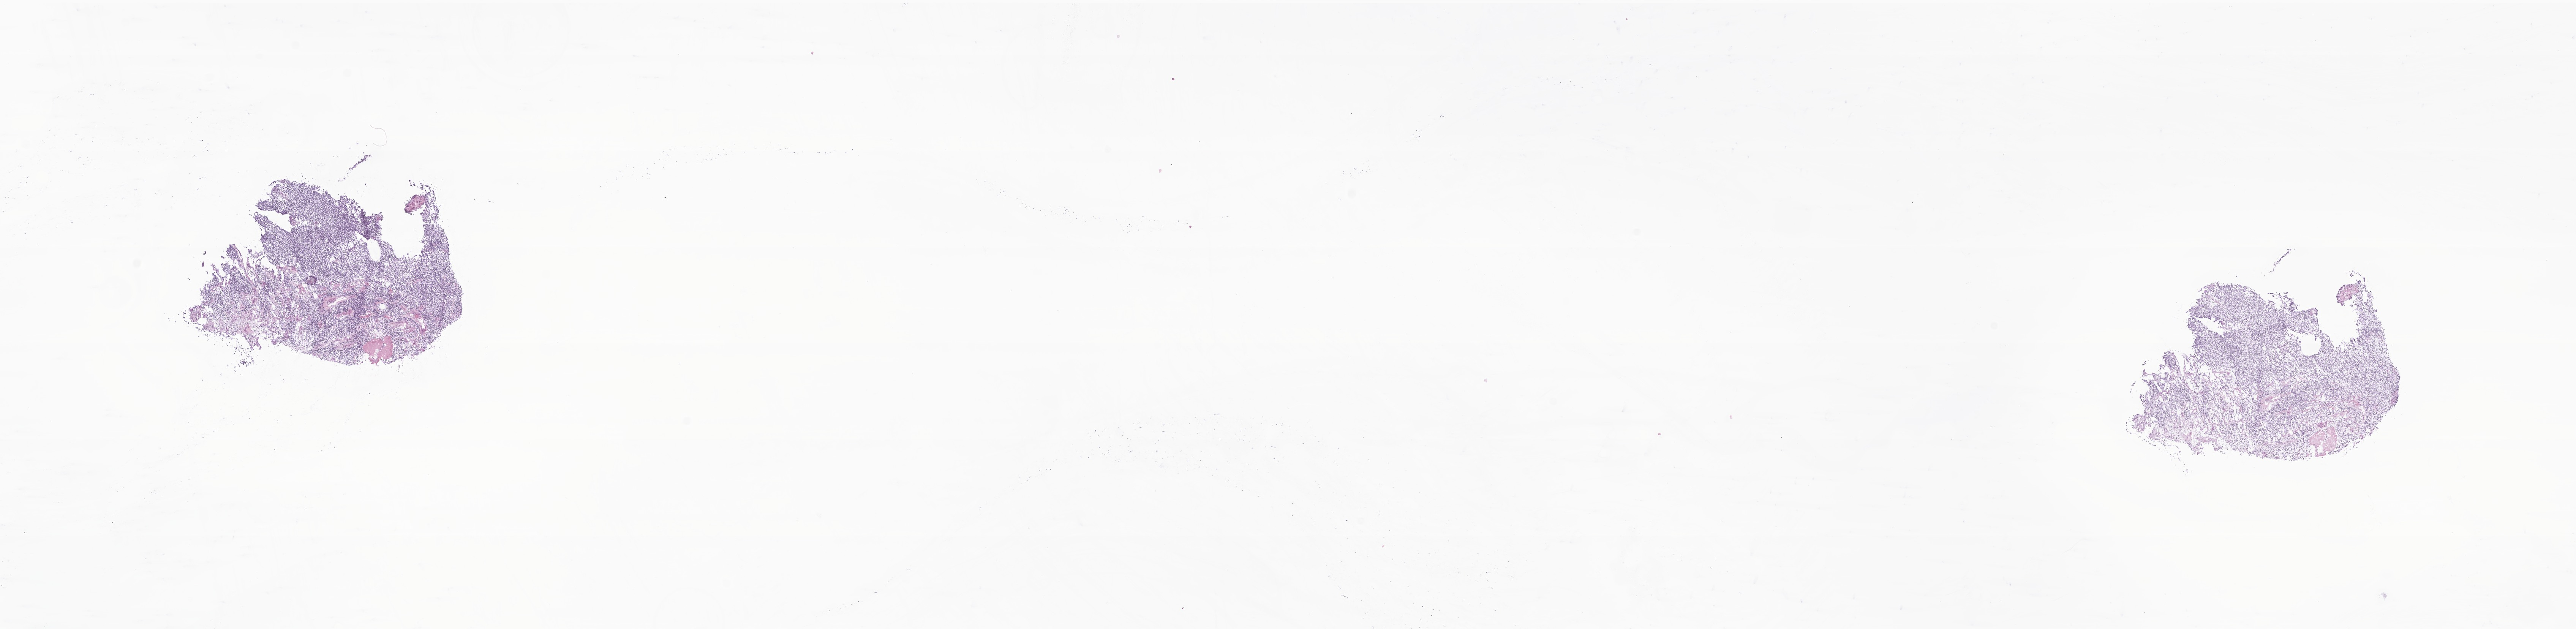
Whole-slide image, hematoxylin and eosin (H&E) stain of tumor tissue from the brain — a low-resolution overview of the entire scanned area, about 28.6 x 7.0 mm, frozen section (OCT-embedded). Female patient, age 827 days (about 2.3 years).
• diagnosis: Medulloblastoma, NOS